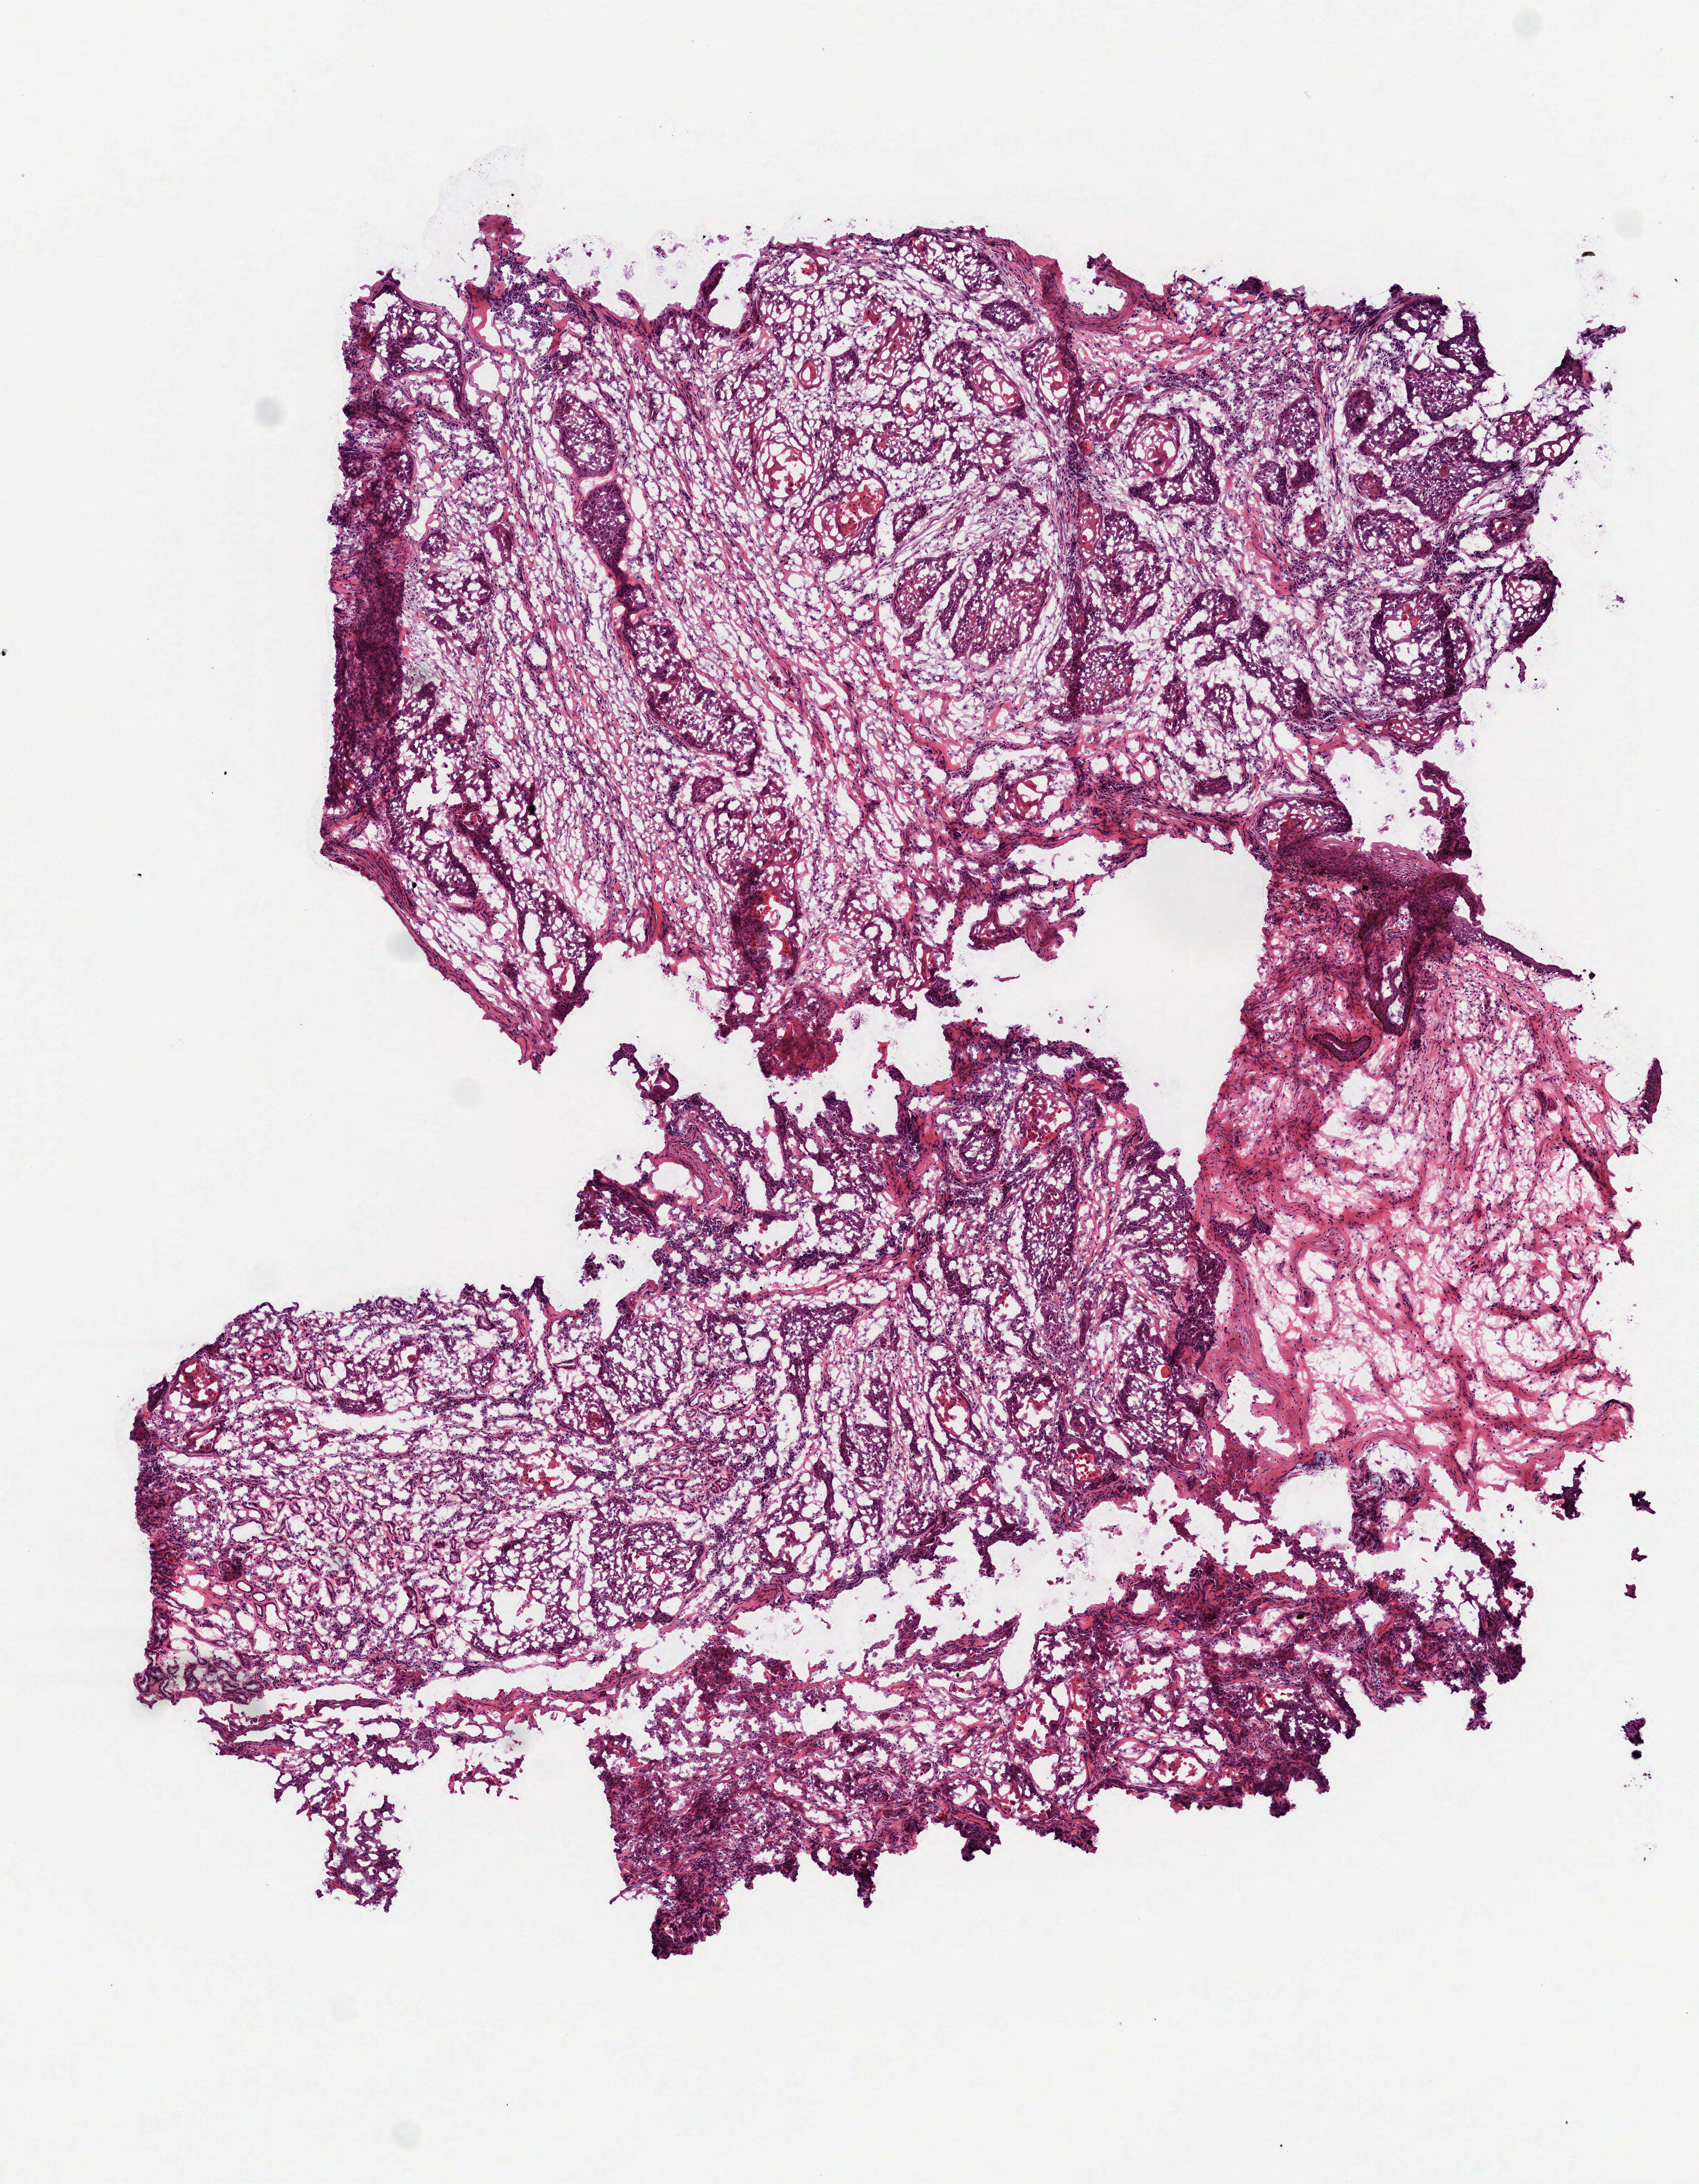
Whole-slide histology image, Hematoxylin and eosin (H&E) stained — a low-resolution overview of the entire scanned area, about 4.8 x 6.2 mm (from a 40x scan). Frozen section from the top of the tissue portion. Head and neck, primary tumour sample. Patient: female, age at initial diagnosis 63 years. Histologic grade: G2 (moderately differentiated). Composition of this section per pathologist review: tumour cells 75%, tumour nuclei 70%, normal cells 0%, stromal cells 25%, necrosis 0%.
Histologic diagnosis: Squamous cell carcinoma, NOS (larynx, NOS). AJCC pathologic stage: IVA (7th edition).